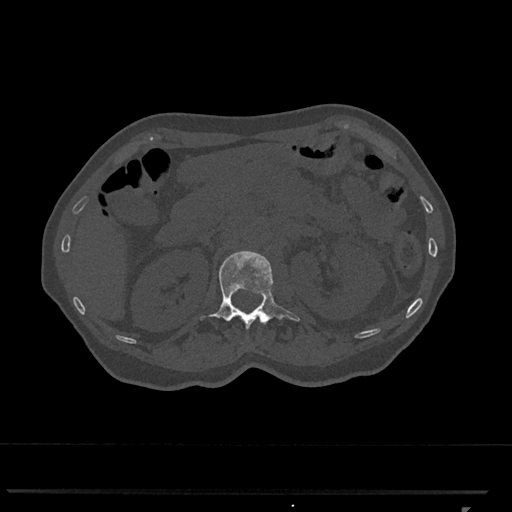
CT including the spine, one axial slice; reconstruction kernel Br40s/3; 120 kVp; bone window (W 1800 / L 400 HU); 0.5 mm slice thickness; 512 × 512 image matrix. Female patient, age 62 years. Case-level facts recorded for this patient, not image findings: primary cancer: renal.
Annotated regions visible in this slice (semi-automatic segmentation, software-assisted and operator-edited):
- L1 vertebra: box from (x=201, y=251) to (x=300, y=330) px